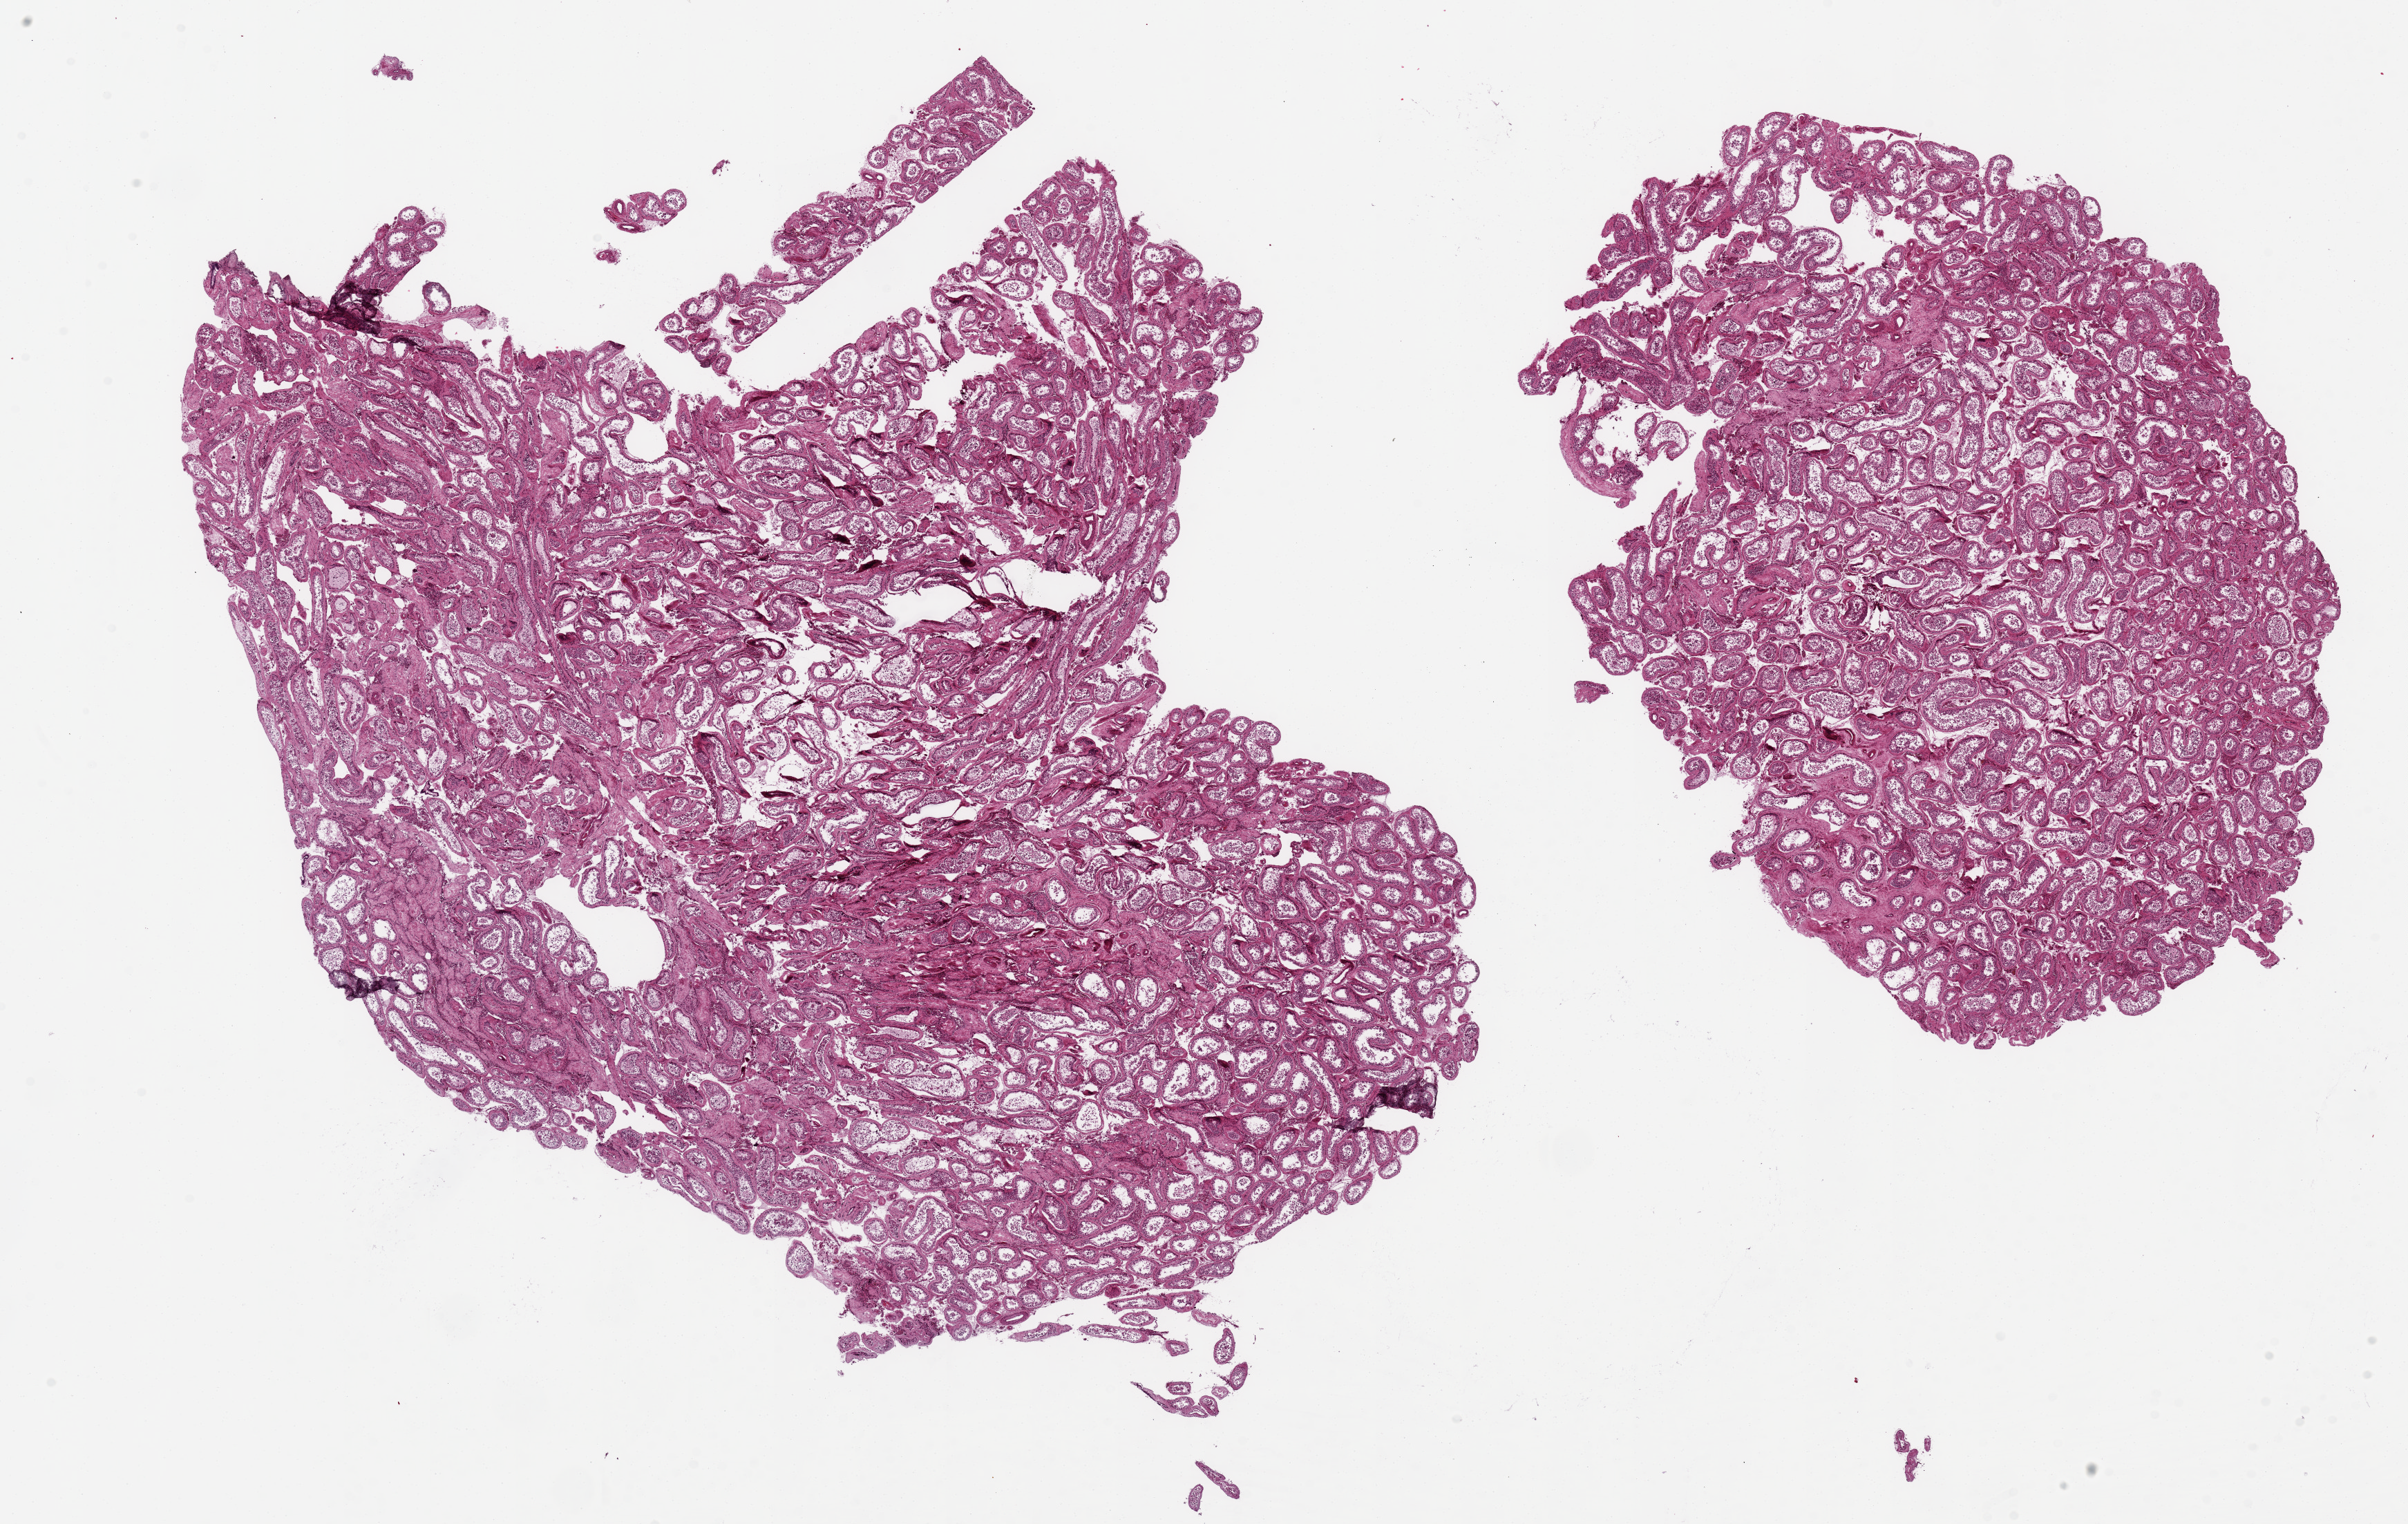
Digitized H&E-stained section, brightfield, whole scanned area (about 27.6 x 17.4 mm, acquisition: 20x scan) shown as a low-resolution overview. PAXgene-fixed, paraffin-embedded tissue. Sampled site (target tissue): testis. Tissue donor sample. Donor: male.
Reviewer comment on this tissue sample: 2 ~11x9mm aliquots. Spermatogenesis is present but appears reduced.